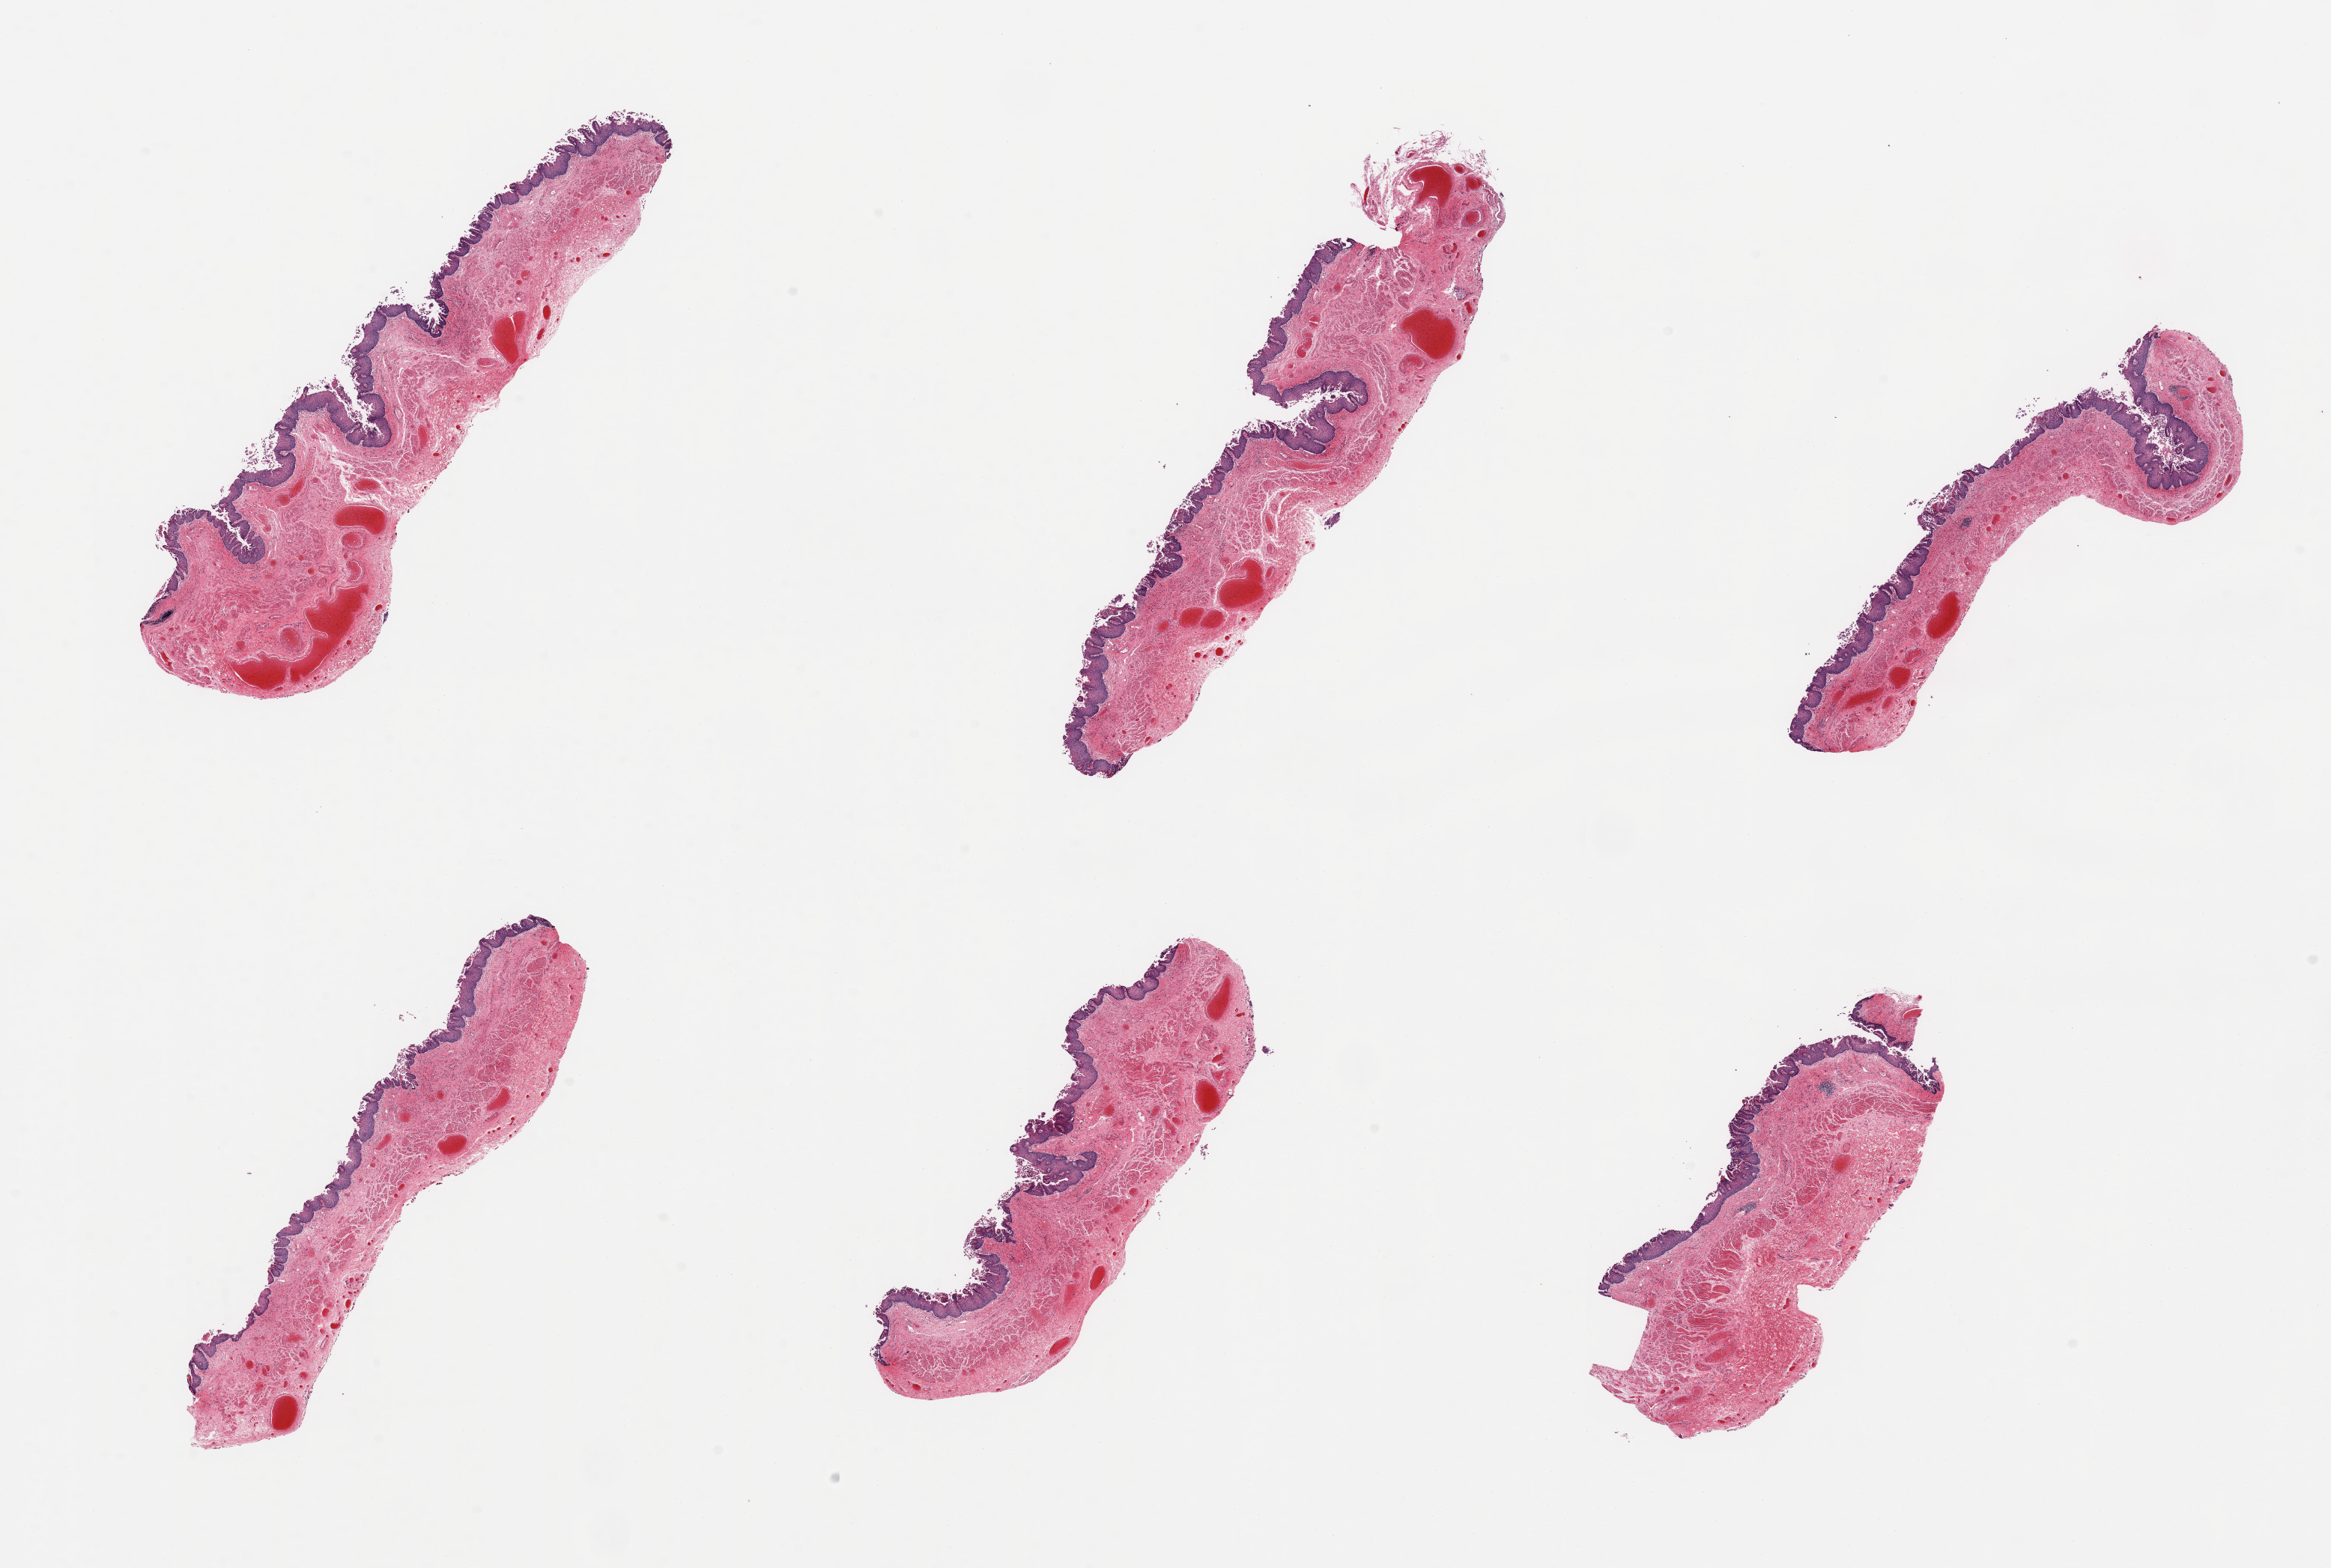
Whole-slide image, haematoxylin and eosin stain — a low-resolution overview of the entire scanned area, about 24.6 x 16.6 mm; PAXgene-fixed, paraffin-embedded tissue; target tissue: esophageal mucous membrane; donor tissue sample.
Review note (as recorded): 6 pieces; squamous epithelium is partially sloughed.